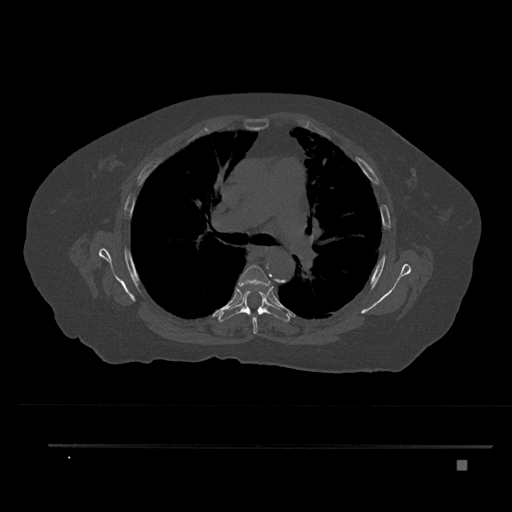
CT including the spine, one axial slice. Position 543 of 797 along the scan axis. Reconstruction kernel Br40s/3. 120 kVp. Bone window (W 1800 / L 400 HU). 0.5 mm slice thickness. 512 × 512 image matrix, field of view 437 × 437 mm. Female patient, age 76 years. Case-level facts recorded for this patient, not image findings: primary cancer: lung; vertebrae with lytic lesions (as recorded): T11, L3.
Structures marked on this image (semi-automatic segmentation, software-assisted and operator-edited):
- T5 vertebra: bounding box [x1, y1, x2, y2] px = [238, 265, 271, 334]
- T6 vertebra: [218, 290, 290, 322]